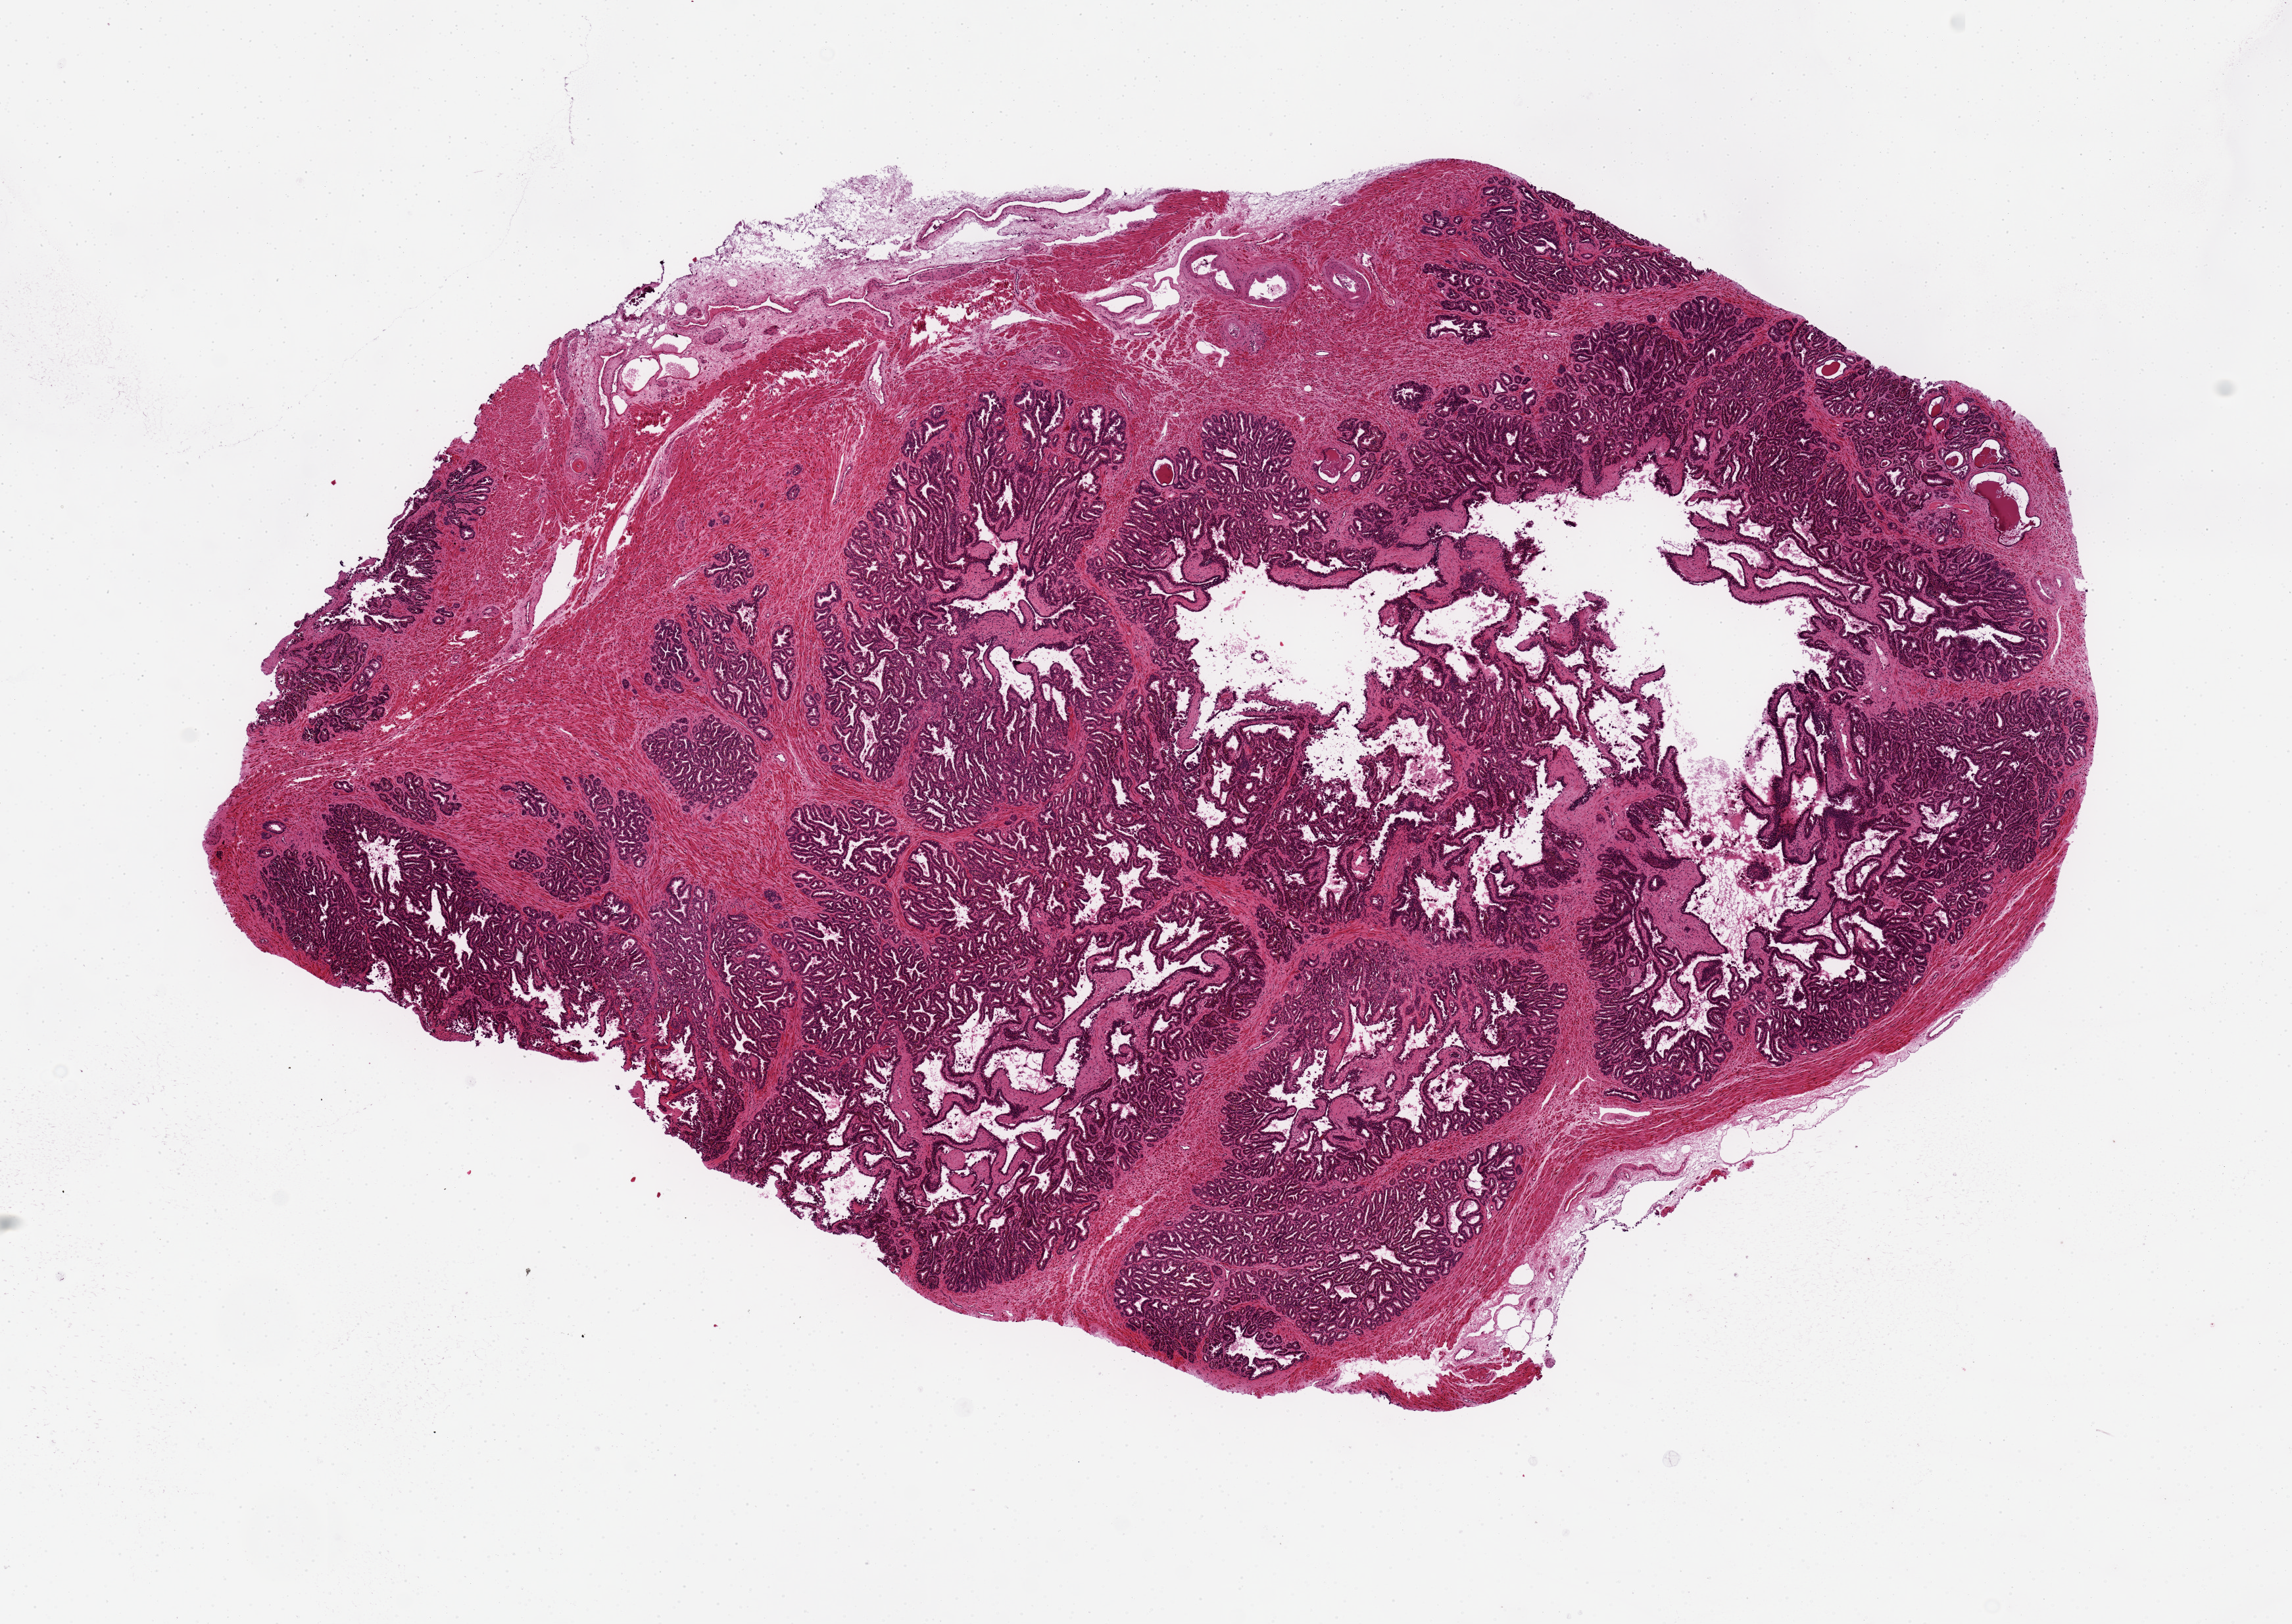
H&E whole-slide image, shown as a low-resolution overview of the whole scanned area (about 13.8 x 9.8 mm, from a 20x scan), PAXgene-fixed, paraffin-embedded tissue, sampled site (target tissue): prostate, donor tissue sample. Male donor.
Pathologist's review note for this sample: Not prostate; seminal vesicle.